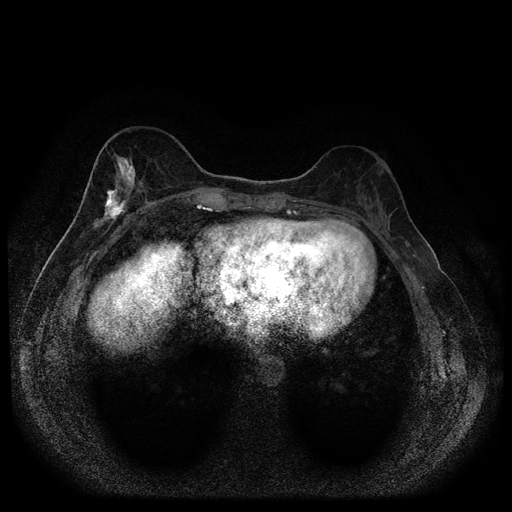
Breast MRI (dynamic contrast-enhanced, multi-phase), one axial slice; position 37 of 116 along the scan axis; dynamic contrast-enhanced series, time point 2 of 5 at this slice position (early post-contrast); 1.5 T; TE 2.7 ms, TR 5.4 ms; 2 mm slice thickness; 512 × 512 image matrix, field of view 330 × 330 mm. Patient: female, 49 years.
Structures marked on this image (semi-automatically segmented with operator editing):
- breast lesion (labelled 'tumour' in the annotation; benign lesions carry a separate 'benign' label): box from (x=90, y=155) to (x=137, y=234) px